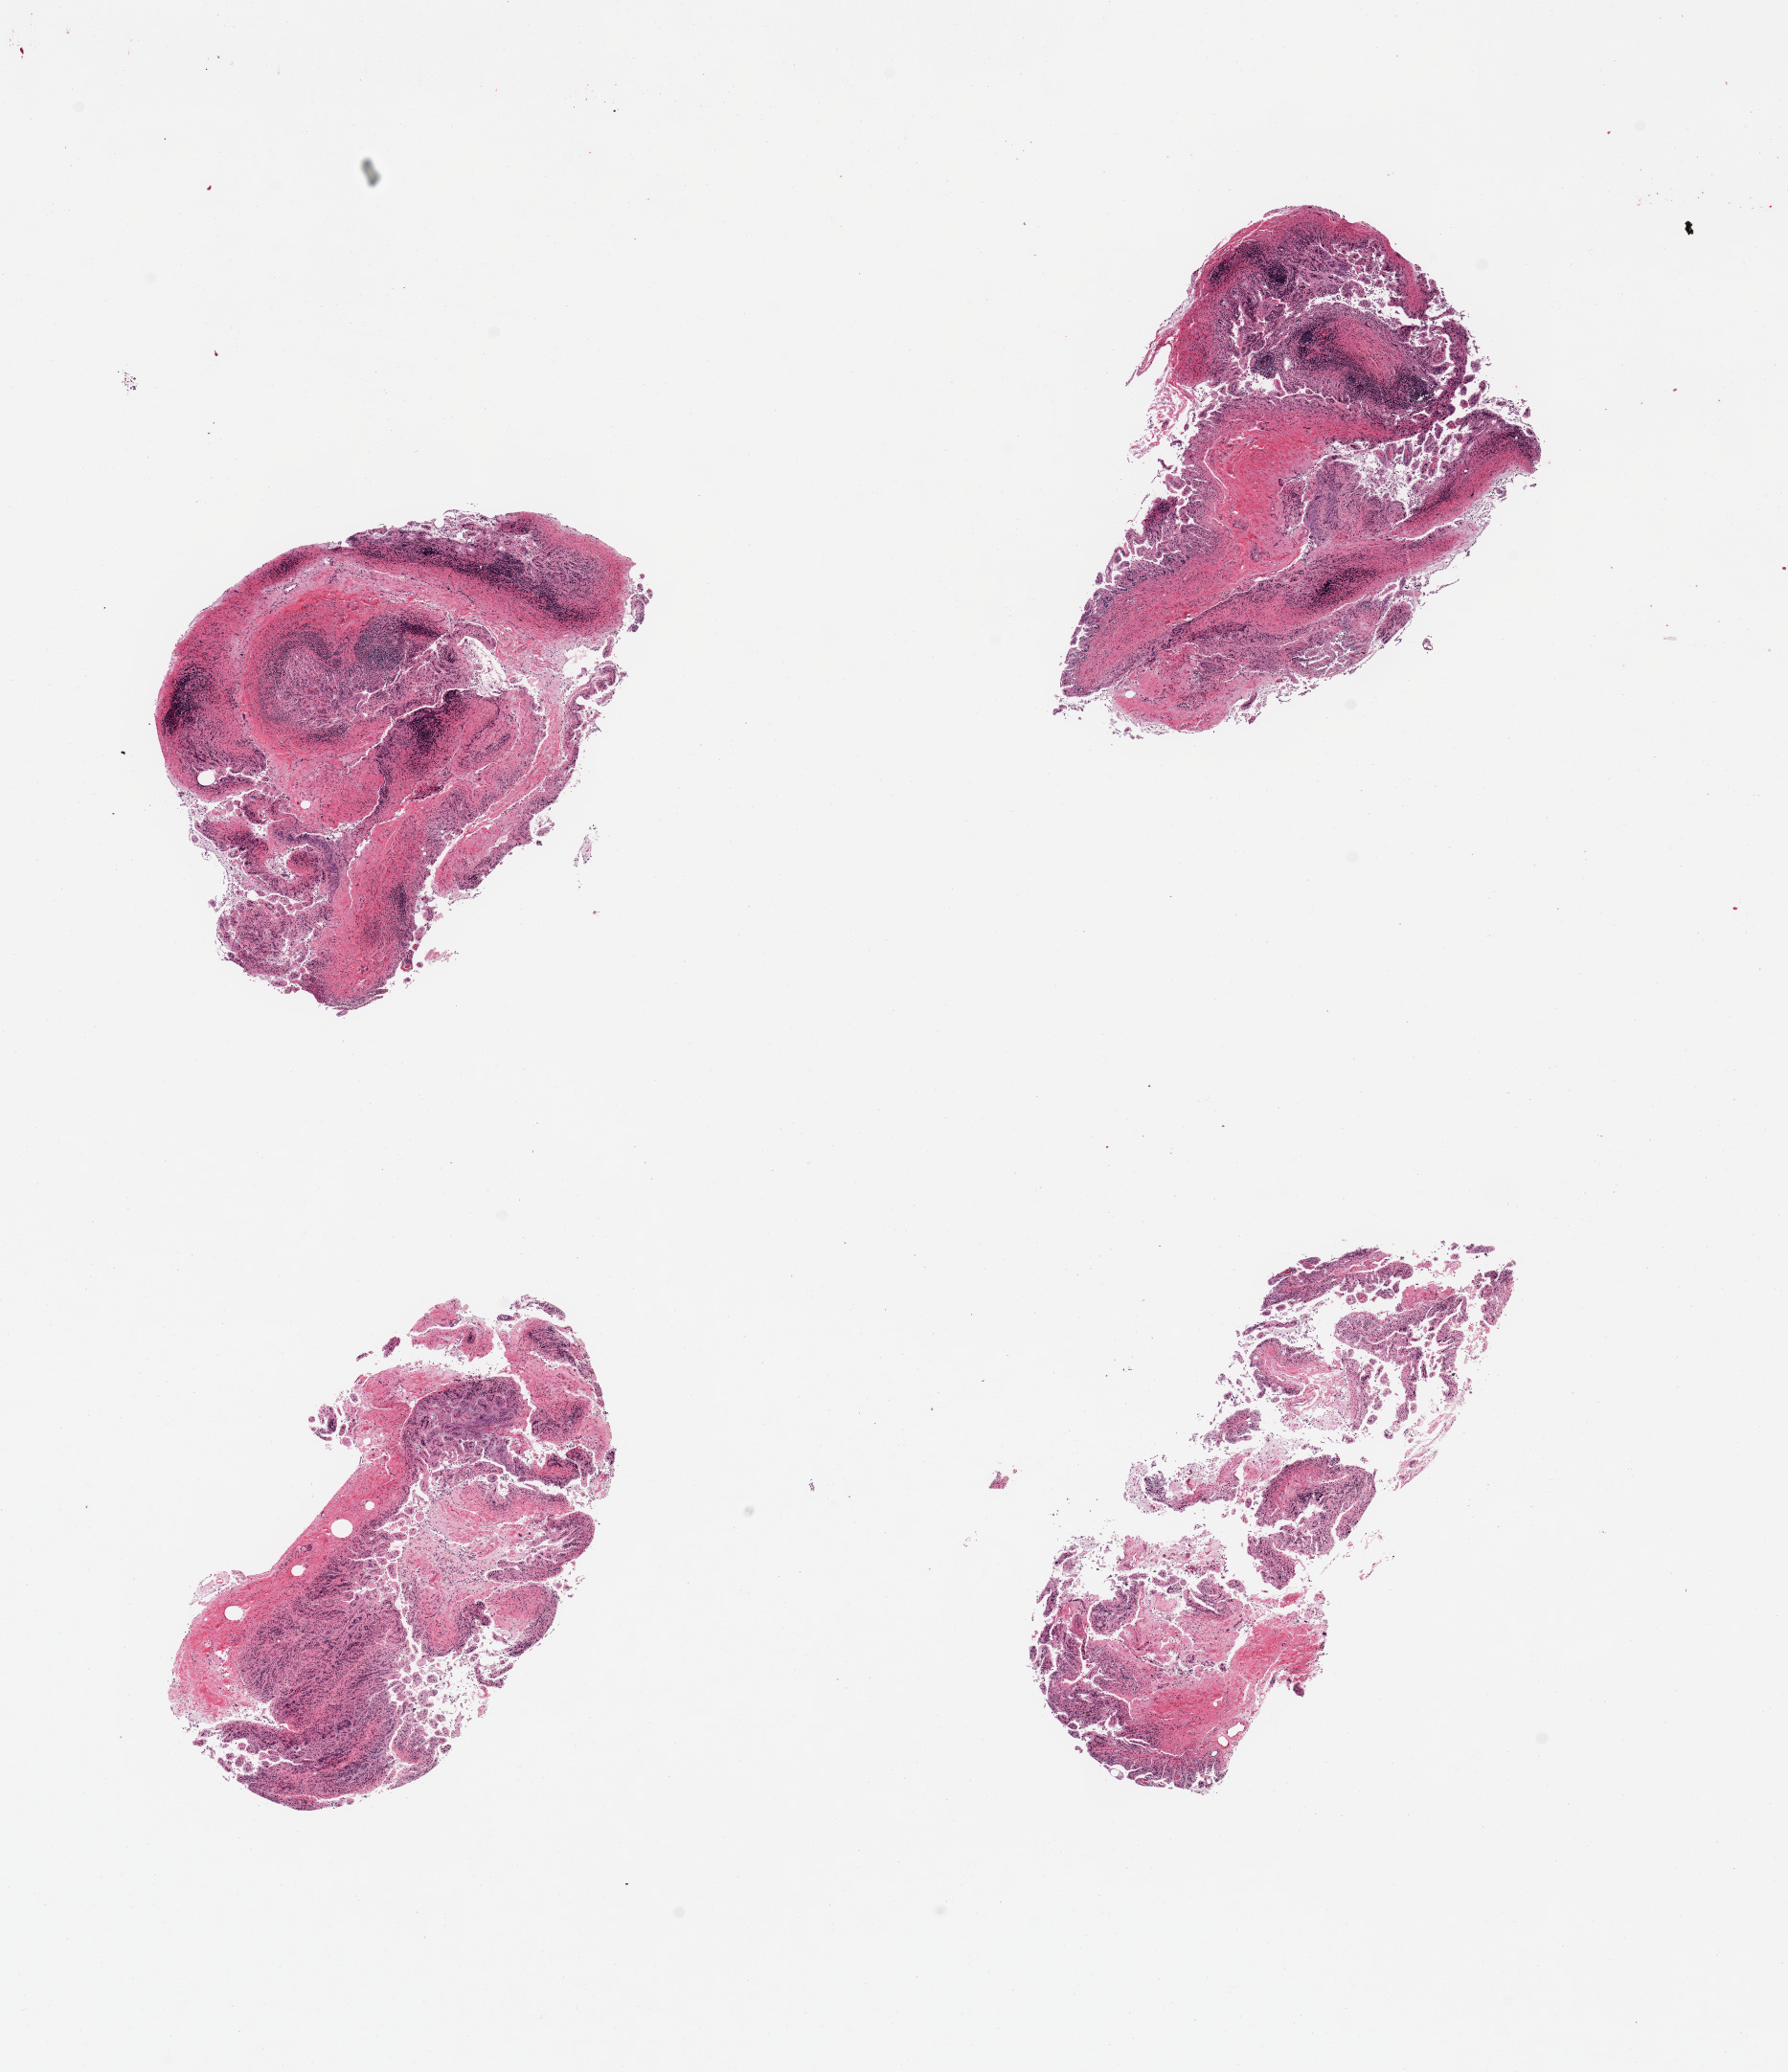
Haematoxylin and eosin whole-slide image — low-resolution overview of the scanned area, about 14.8 x 17.1 mm; PAXgene-fixed, paraffin-embedded tissue; section of ileum (target tissue); tissue donor sample. Female donor.
Pathologist's review note for this sample: 4 pieces; well dissected, but too autolyzed.